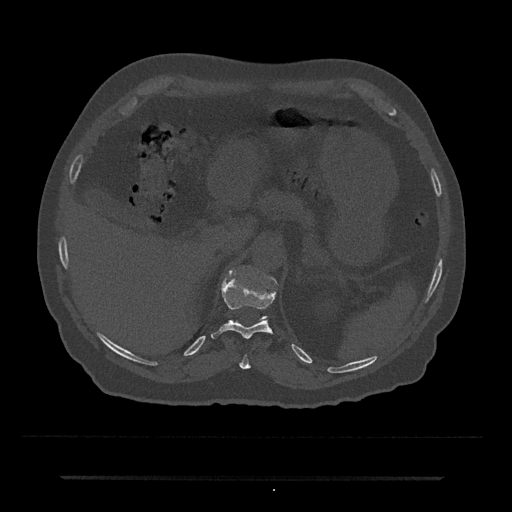
CT including the spine, one axial slice. Position 177 of 797 along the scan axis. Reconstruction kernel Br40s/3. Bone window (W 1800 / L 400 HU). 0.5 mm slice thickness. 512 × 512 image matrix, field of view 437 × 437 mm. Male patient, age 69 years. From the clinical record (not read from this slice): primary cancer: prostate.
Outlined on this slice (semi-automatically segmented with operator editing):
- T10 vertebra: box from (x=239, y=355) to (x=251, y=369) px
- T11 vertebra: (x=211, y=275)–(x=282, y=339)
- T12 vertebra: (x=263, y=277)–(x=276, y=319)